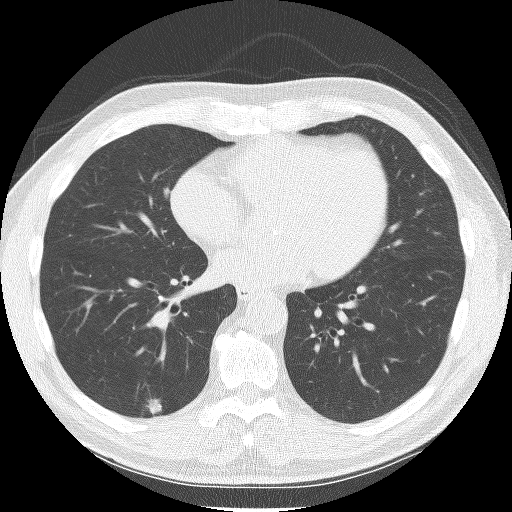
Low-dose screening chest CT, one axial slice. Position 65 of 150 along the scan axis. 120 kVp. Lung window (W 1500 / L -600 HU). 2.5 mm slice thickness. 512 × 512 image matrix, field of view 335 × 335 mm.
Annotated regions visible in this slice (outlined manually by an expert reader):
- lesion 1 (tumor, lower lobe of right lung): box from (x=145, y=398) to (x=162, y=415) px